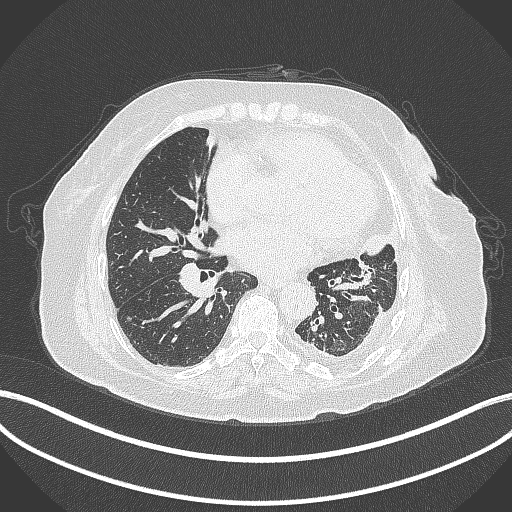
Chest CT, one axial slice; slice 163 of 399 in the series (ordered by position); reconstruction kernel B70f; 120 kVp; lung window (W 1500 / L -600 HU); 1 mm slice thickness; 512 × 512 image matrix, field of view 400 × 400 mm. Patient: female, 75 years. Case-level facts recorded for this patient, not image findings: clinical TNM (as recorded): T3 N3 M1.
Outlined on this slice (bounding box drawn by a radiologist):
- lung tumour (recorded histology: adenocarcinoma): box from (x=357, y=225) to (x=395, y=264) px